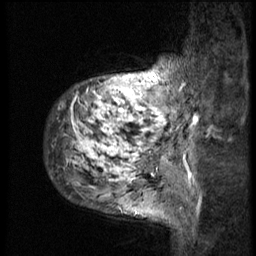
Breast MRI (dynamic contrast-enhanced), one sagittal slice. Slice 9 of 58 in the series (ordered by position). 3 images stored at this slice position (order not interpretable as contrast timing). 1.5 T. TE 4.2 ms, TR 9 ms. 2.5 mm slice thickness. 256 × 256 image matrix, field of view 180 × 180 mm. Patient: female, 50 years. From the clinical record (not read from this slice): setting: breast cancer imaged before/during neoadjuvant chemotherapy; receptor status: triple-negative.
Outlined on this slice (semi-automatically segmented with operator editing):
- analysis volume of interest (the breast-tissue region the enhancement analysis was run in; not a lesion): bounding box [x1, y1, x2, y2] px = [46, 49, 186, 214]
- tumour enhancement mask (voxels above the 140 % enhancement threshold inside the analysis volume of interest): [60, 72, 169, 187]